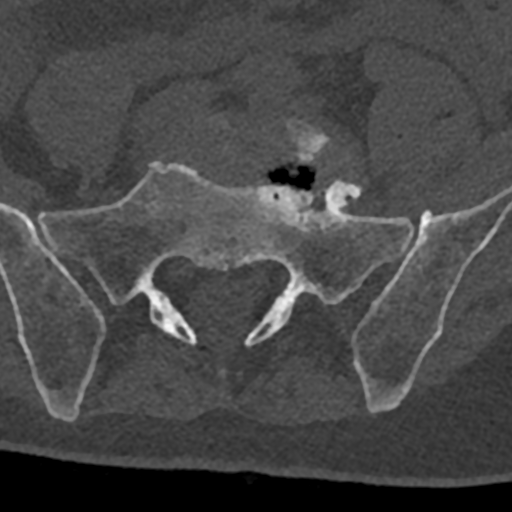
CT including the spine, one axial slice; slice 152 of 797 in the series (ordered by position); 120 kVp; bone window (W 1800 / L 400 HU); 0.5 mm slice thickness; 512 × 512 image matrix, field of view 160 × 160 mm. Male patient, age 74 years. Case-level facts recorded for this patient, not image findings: primary cancer: renal; vertebrae with lytic lesions (as recorded): T10, L1, L2, L3, L4, L5.
Outlined on this slice (semi-automatic segmentation, software-assisted and operator-edited):
- L5 vertebra: bounding box [x1, y1, x2, y2] px = [219, 120, 331, 164]